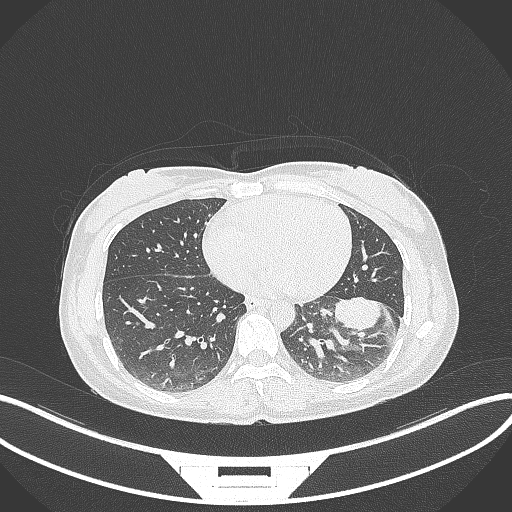
Chest CT, one axial slice; slice 20 of 244 in the series (ordered by position); reconstruction kernel B70f; lung window (W 1500 / L -600 HU); 1 mm slice thickness; 512 × 512 image matrix, field of view 400 × 400 mm. Female patient, age 41 years. Case-level facts recorded for this patient, not image findings: clinical TNM (as recorded): T2a N3 M1b.
Outlined on this slice (rectangle marked by the reading radiologist):
- lung tumour (recorded histology: adenocarcinoma): bounding box <332,296,382,331> (left, top, right, bottom; pixels)